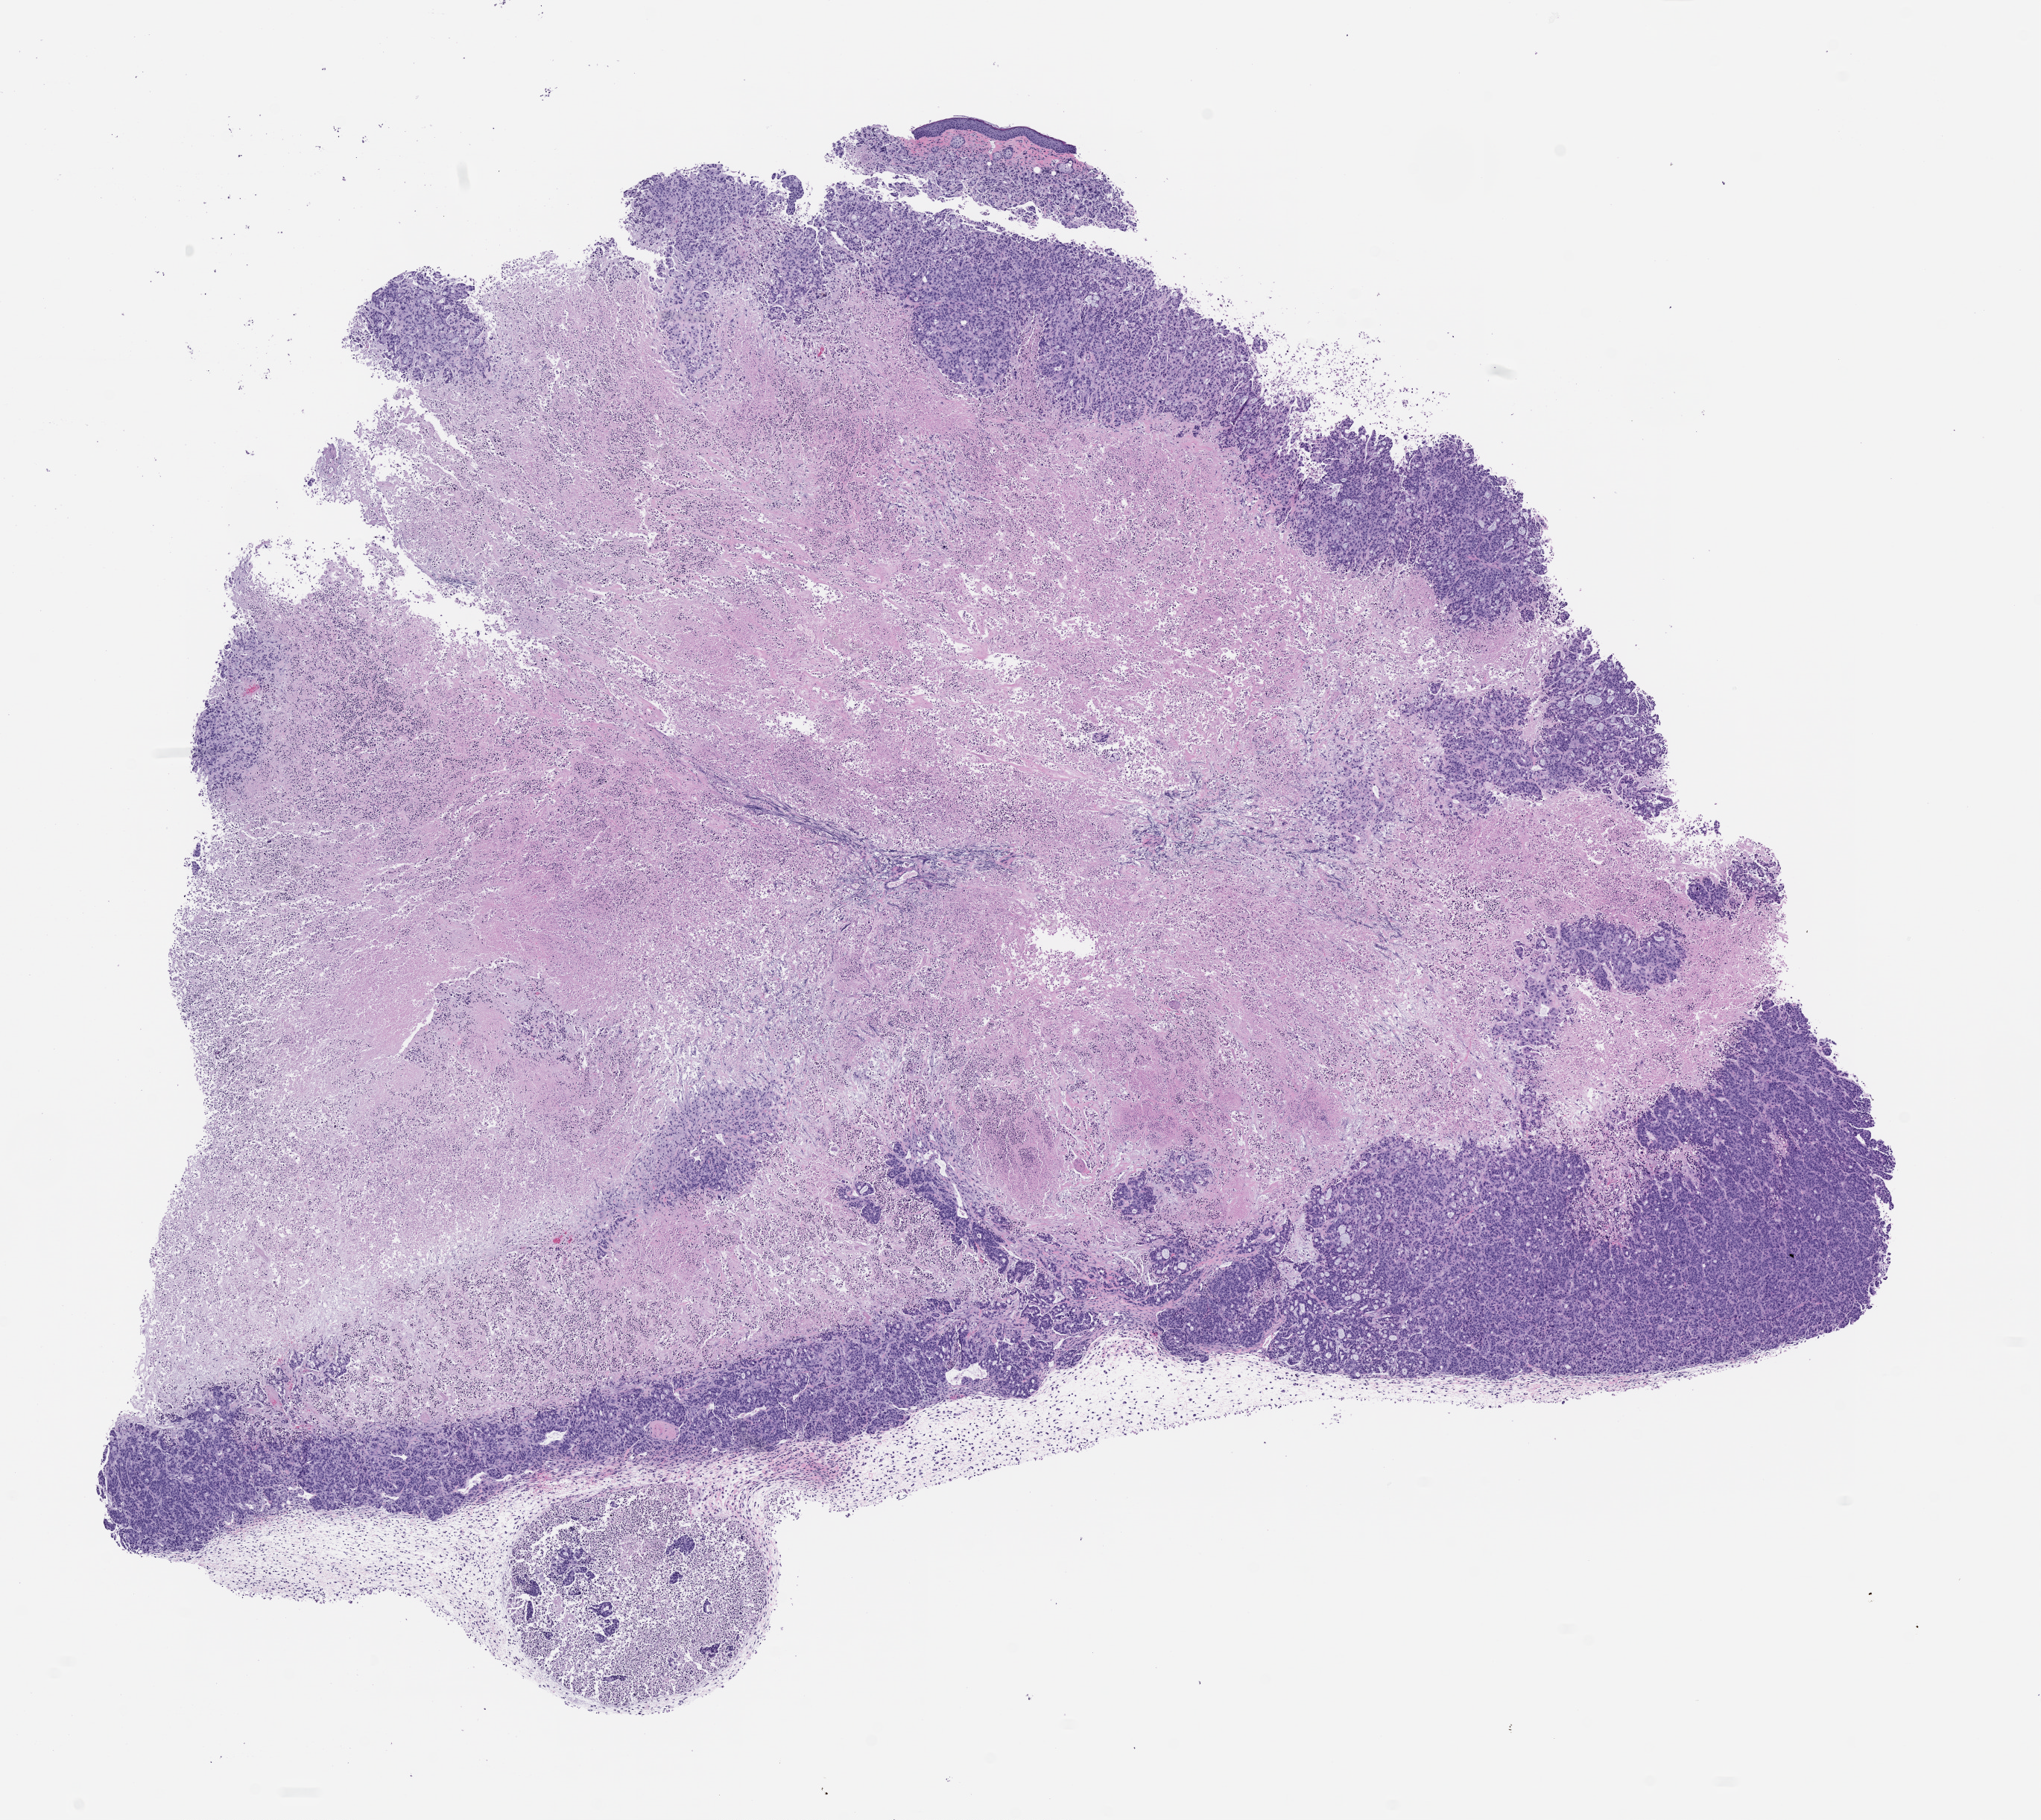
Whole-slide image, H&E: patient-derived xenograft (human tumor grown in a mouse), passage 2, low-resolution overview of the scanned area, about 11.0 x 9.8 mm, formalin-fixed paraffin-embedded section, tumor site category: colon.
Originating patient diagnosis: Colon Adenocarcinoma.